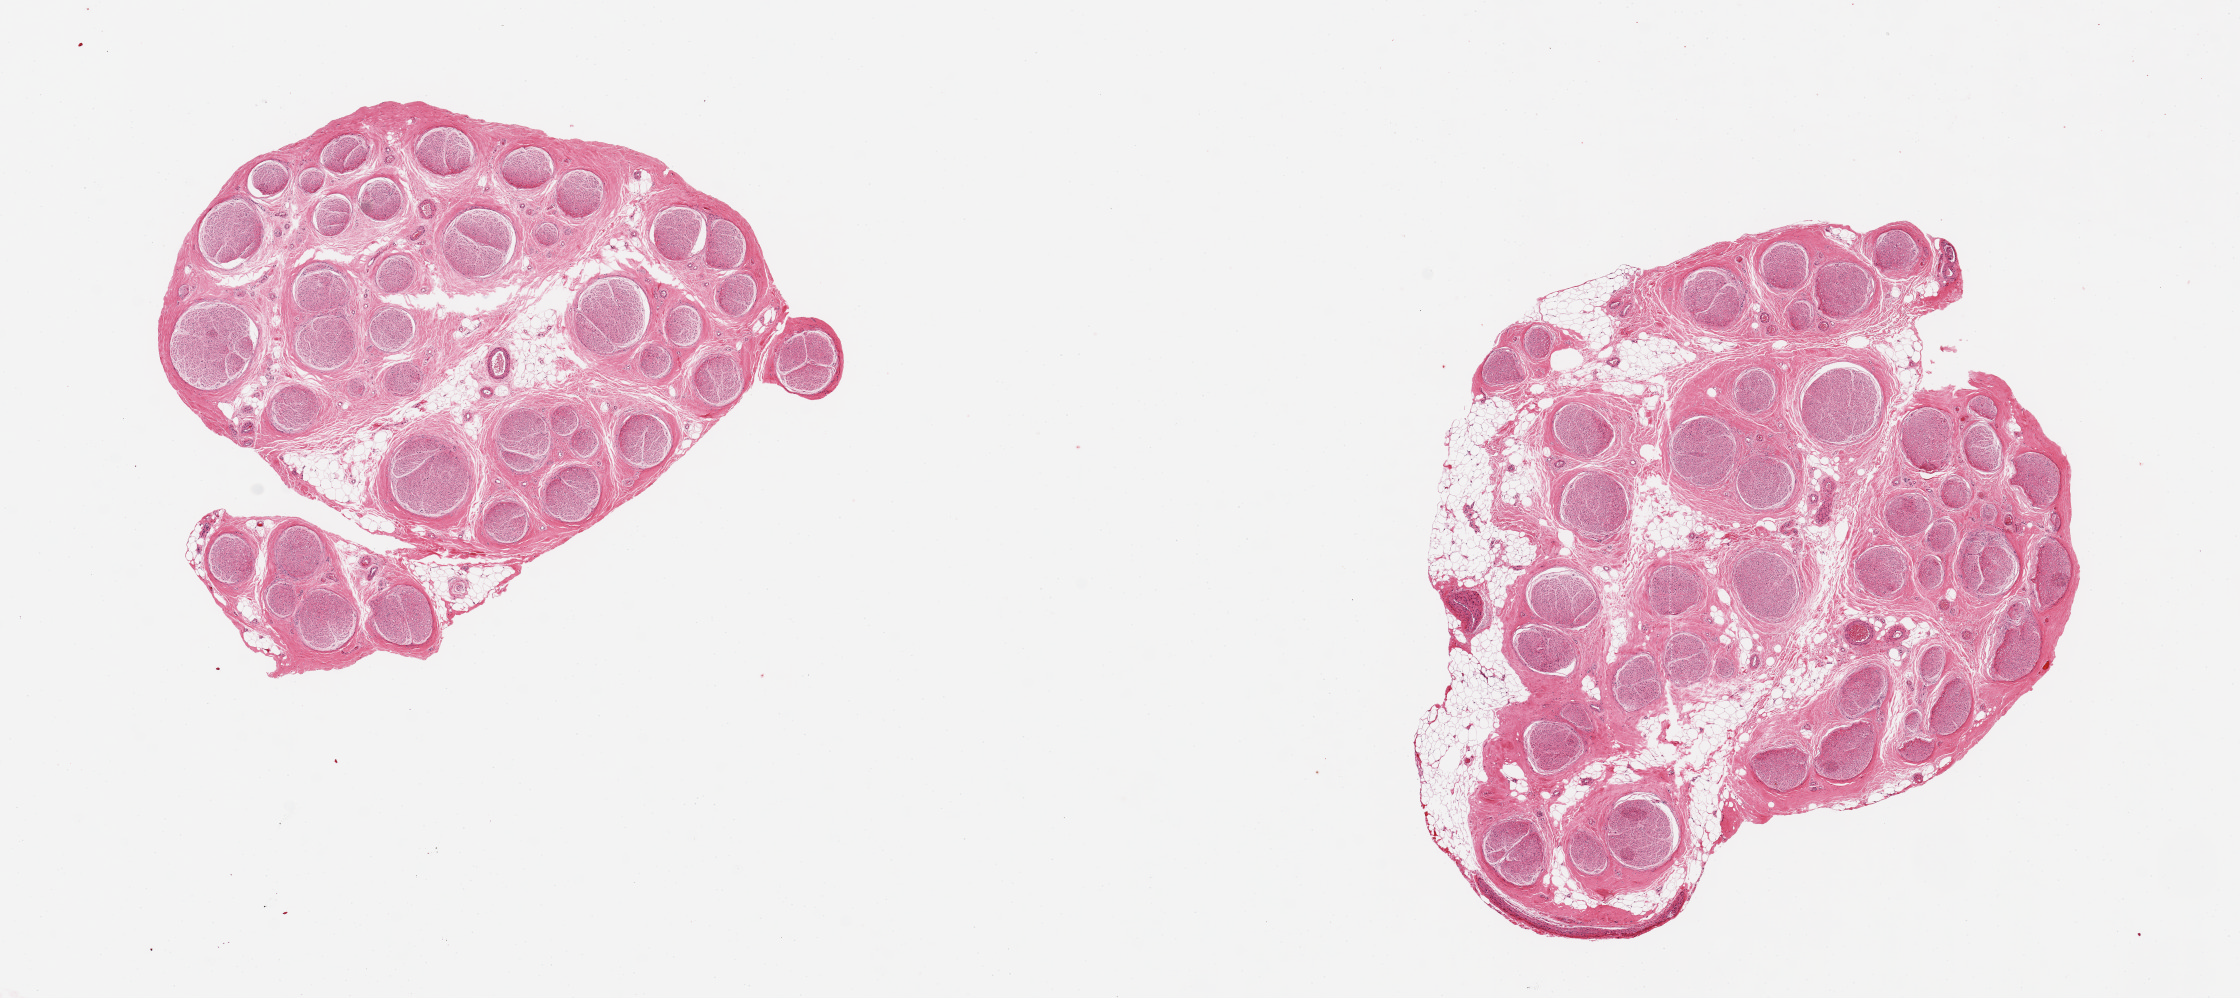
Whole-slide image, H&E stain — low-resolution overview of the scanned area, about 17.7 x 7.9 mm, PAXgene-fixed paraffin-embedded (PFPE) section, section of tibial nerve (target tissue), tissue donor sample. Donor sex: male.
• reviewer comment on this tissue sample: 2 pieces